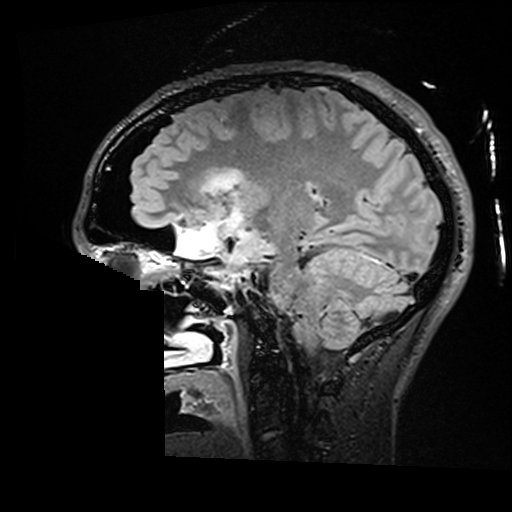
Brain MRI from a brain-tumour surgery series, one sagittal slice. T2 FLAIR. 512 × 512 image matrix, field of view 250 × 250 mm. Case-level facts recorded for this patient, not image findings: histopathology: Astrocytoma; WHO grade: 2; IDH mutation: yes; tumour location: Right Insular.
Outlined on this slice (manually delineated by an expert):
- residual tumour: bounding box (x1, y1, x2, y2) in pixels: (206, 171, 244, 192)